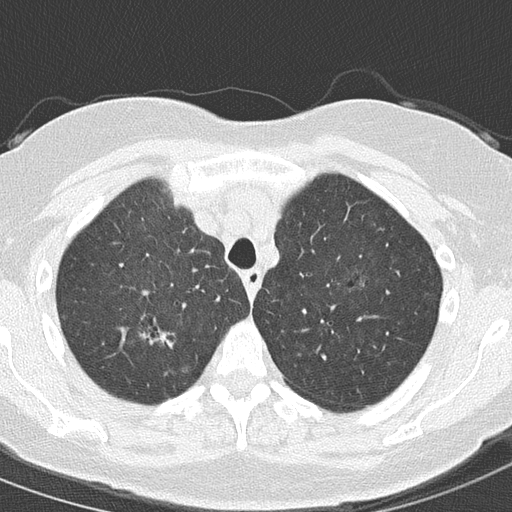
Axial slice from a low-dose chest CT screening exam, second annual screen, lung window (W 1500 / L -600 HU), lung (sharp) reconstruction kernel (B50f), slice 35 of 157 in the series, 512 × 512 image matrix. Female, age 61 years at enrolment. Current smoker at enrolment.
Expert-annotated lung lesion, bounding box (x1, y1, x2, y2) in pixels: (144, 315, 186, 355). Screening reader's record for this exam (one nodule recorded; not confirmed to be the boxed lesion): non-calcified nodule or mass ≥4 mm, right upper lobe, 15 × 10 mm, spiculated (stellate) margins, ground glass attenuation, pre-existing on the prior screen: yes; interval growth: yes. Participant outcome: lung cancer diagnosed 91 days after this screen — adenocarcinoma, NOS, right upper lobe, moderately differentiated (G2), stage IA (AJCC 6th edition), 20 mm at pathology.